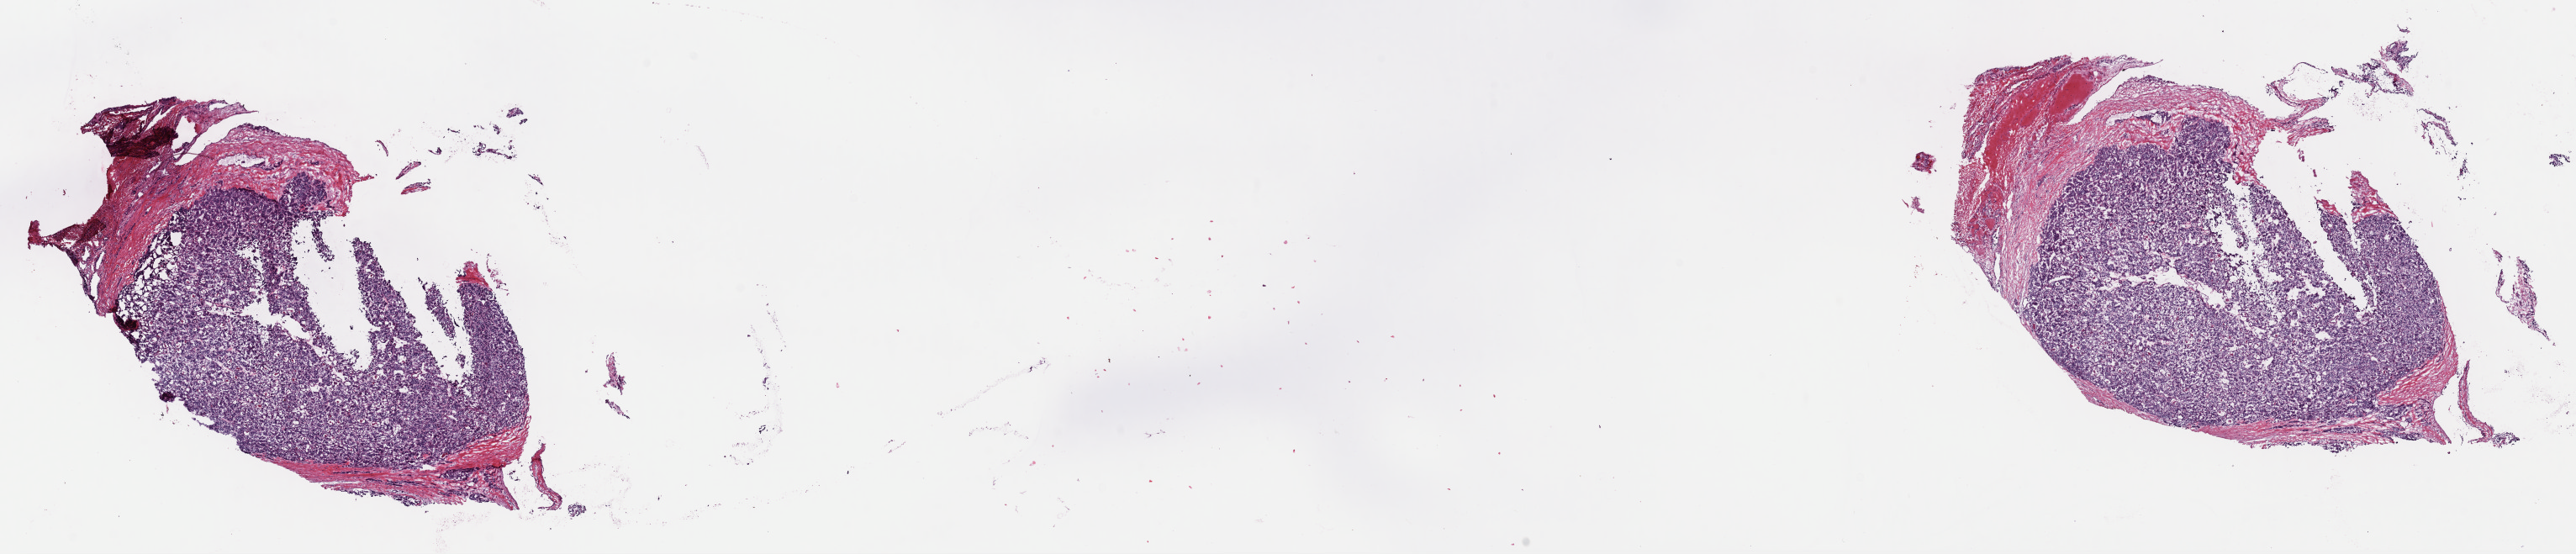
Digitized H&E tissue section (whole slide), shown as a low-resolution overview of the whole scanned area (about 24.2 x 5.2 mm, acquisition: 40x scan); frozen section from the top of the tissue portion; sample: primary tumour, thyroid. Patient: female, age at initial diagnosis 24 years. Pathologist review of this section (percent, as recorded): tumour cells 80%, tumour nuclei 92%, normal cells 0%, stromal cells 20%, necrosis 0%. Infiltration values recorded for this section: lymphocyte infiltration 0%, monocyte infiltration 0%, neutrophil infiltration 0%.
Laterality: left. Lymph nodes positive (case pathology): 0 of 3 examined. Histologic diagnosis: Papillary adenocarcinoma, NOS (thyroid gland). AJCC pathologic stage: I.